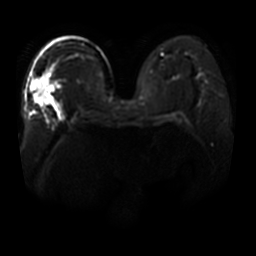
Breast MRI, one axial slice. Slice 25 of 44 in the series (ordered by position). Diffusion-weighted series; image 2 of 4 stored at this slice position (different b-values; order by instance number). 3 T. 256 × 256 image matrix, field of view 400 × 400 mm. Female patient.
Structures marked on this image (manually delineated by an expert):
- tumour on diffusion-weighted imaging: bounding box <32,77,53,106> (left, top, right, bottom; pixels)